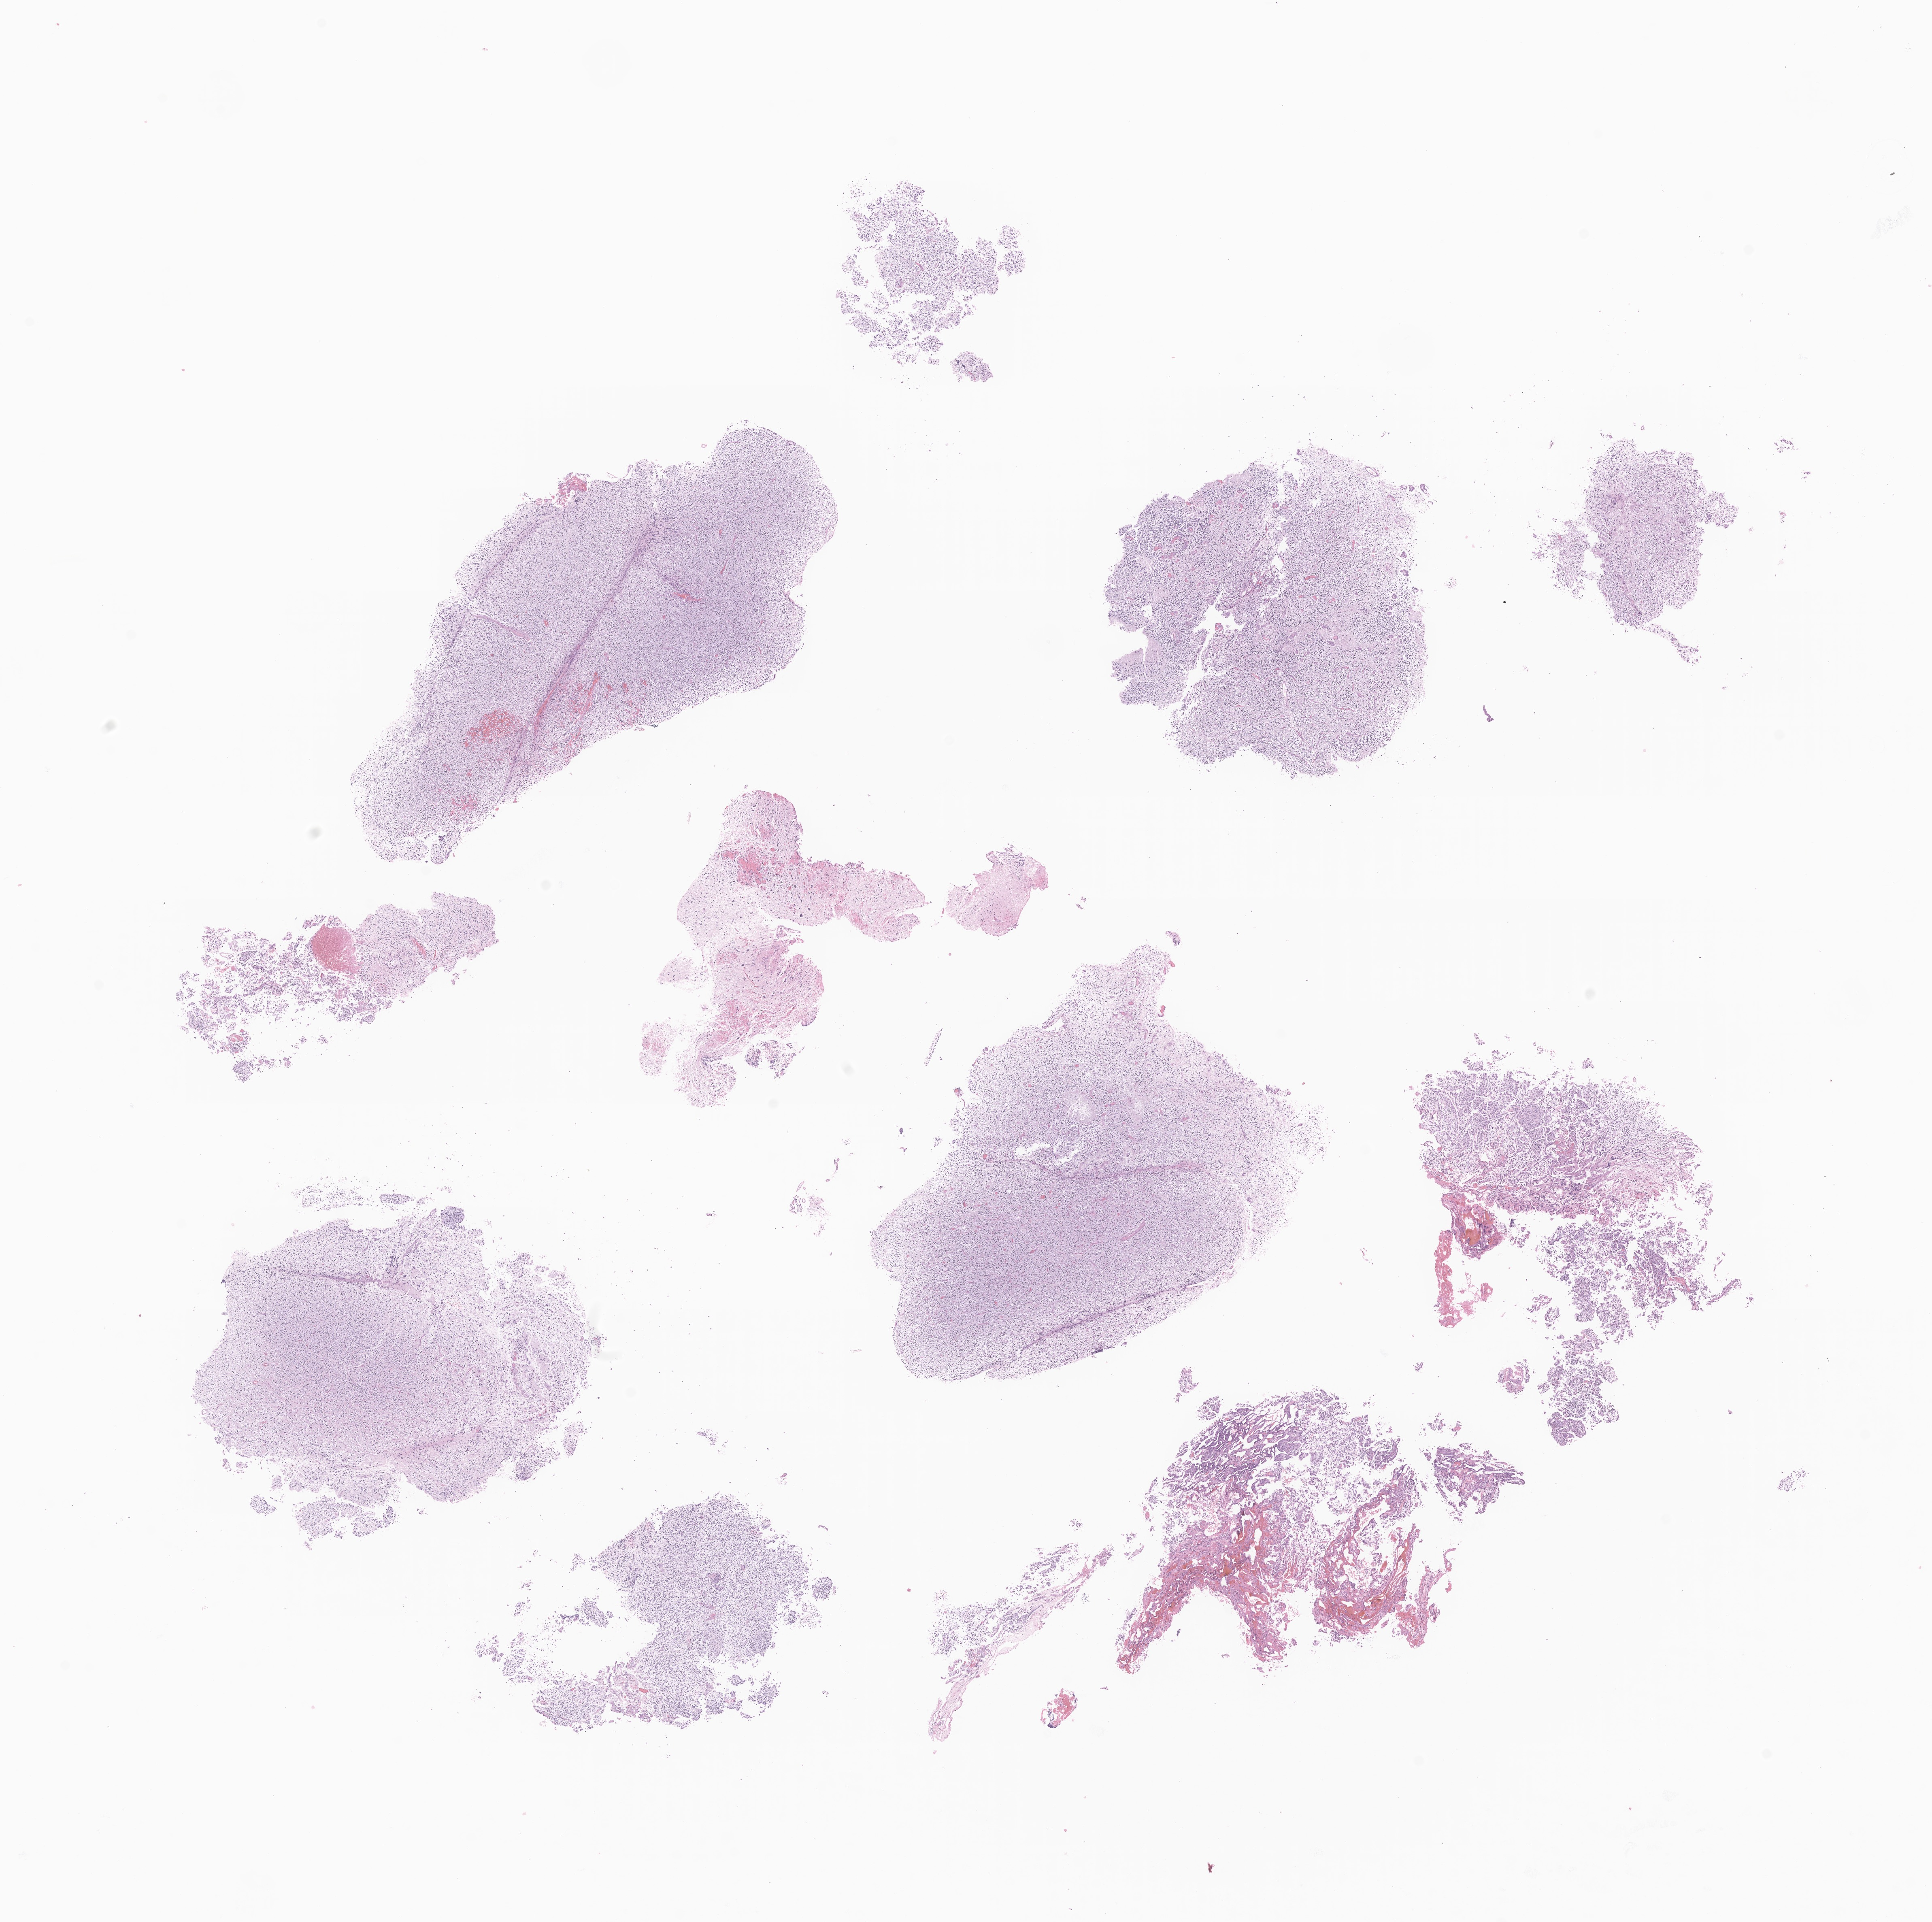
H&E whole-slide image of tumor tissue from the brain — a low-resolution overview of the entire scanned area, about 20.1 x 20.0 mm. Formalin-fixed, paraffin-embedded (FFPE) tissue. Patient: male, age 139 months (11 years 7 months).
Diagnosis (ICD-O-3 morphology term): Neoplasm, uncertain whether benign or malignant.